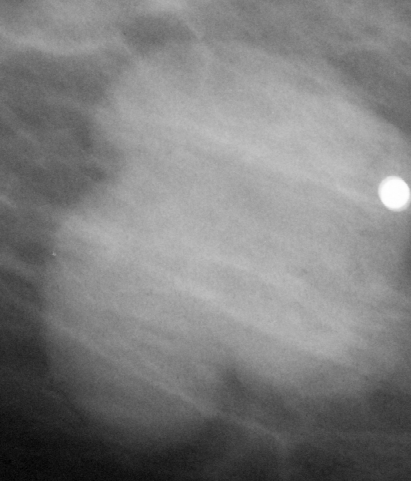
Crop from a digitized film mammogram around one marked abnormality, left breast, MLO view.
Finding: mass, shape lobulated, margins circumscribed; BI-RADS assessment category 5; pathology result (as recorded, not read from the image): malignant.